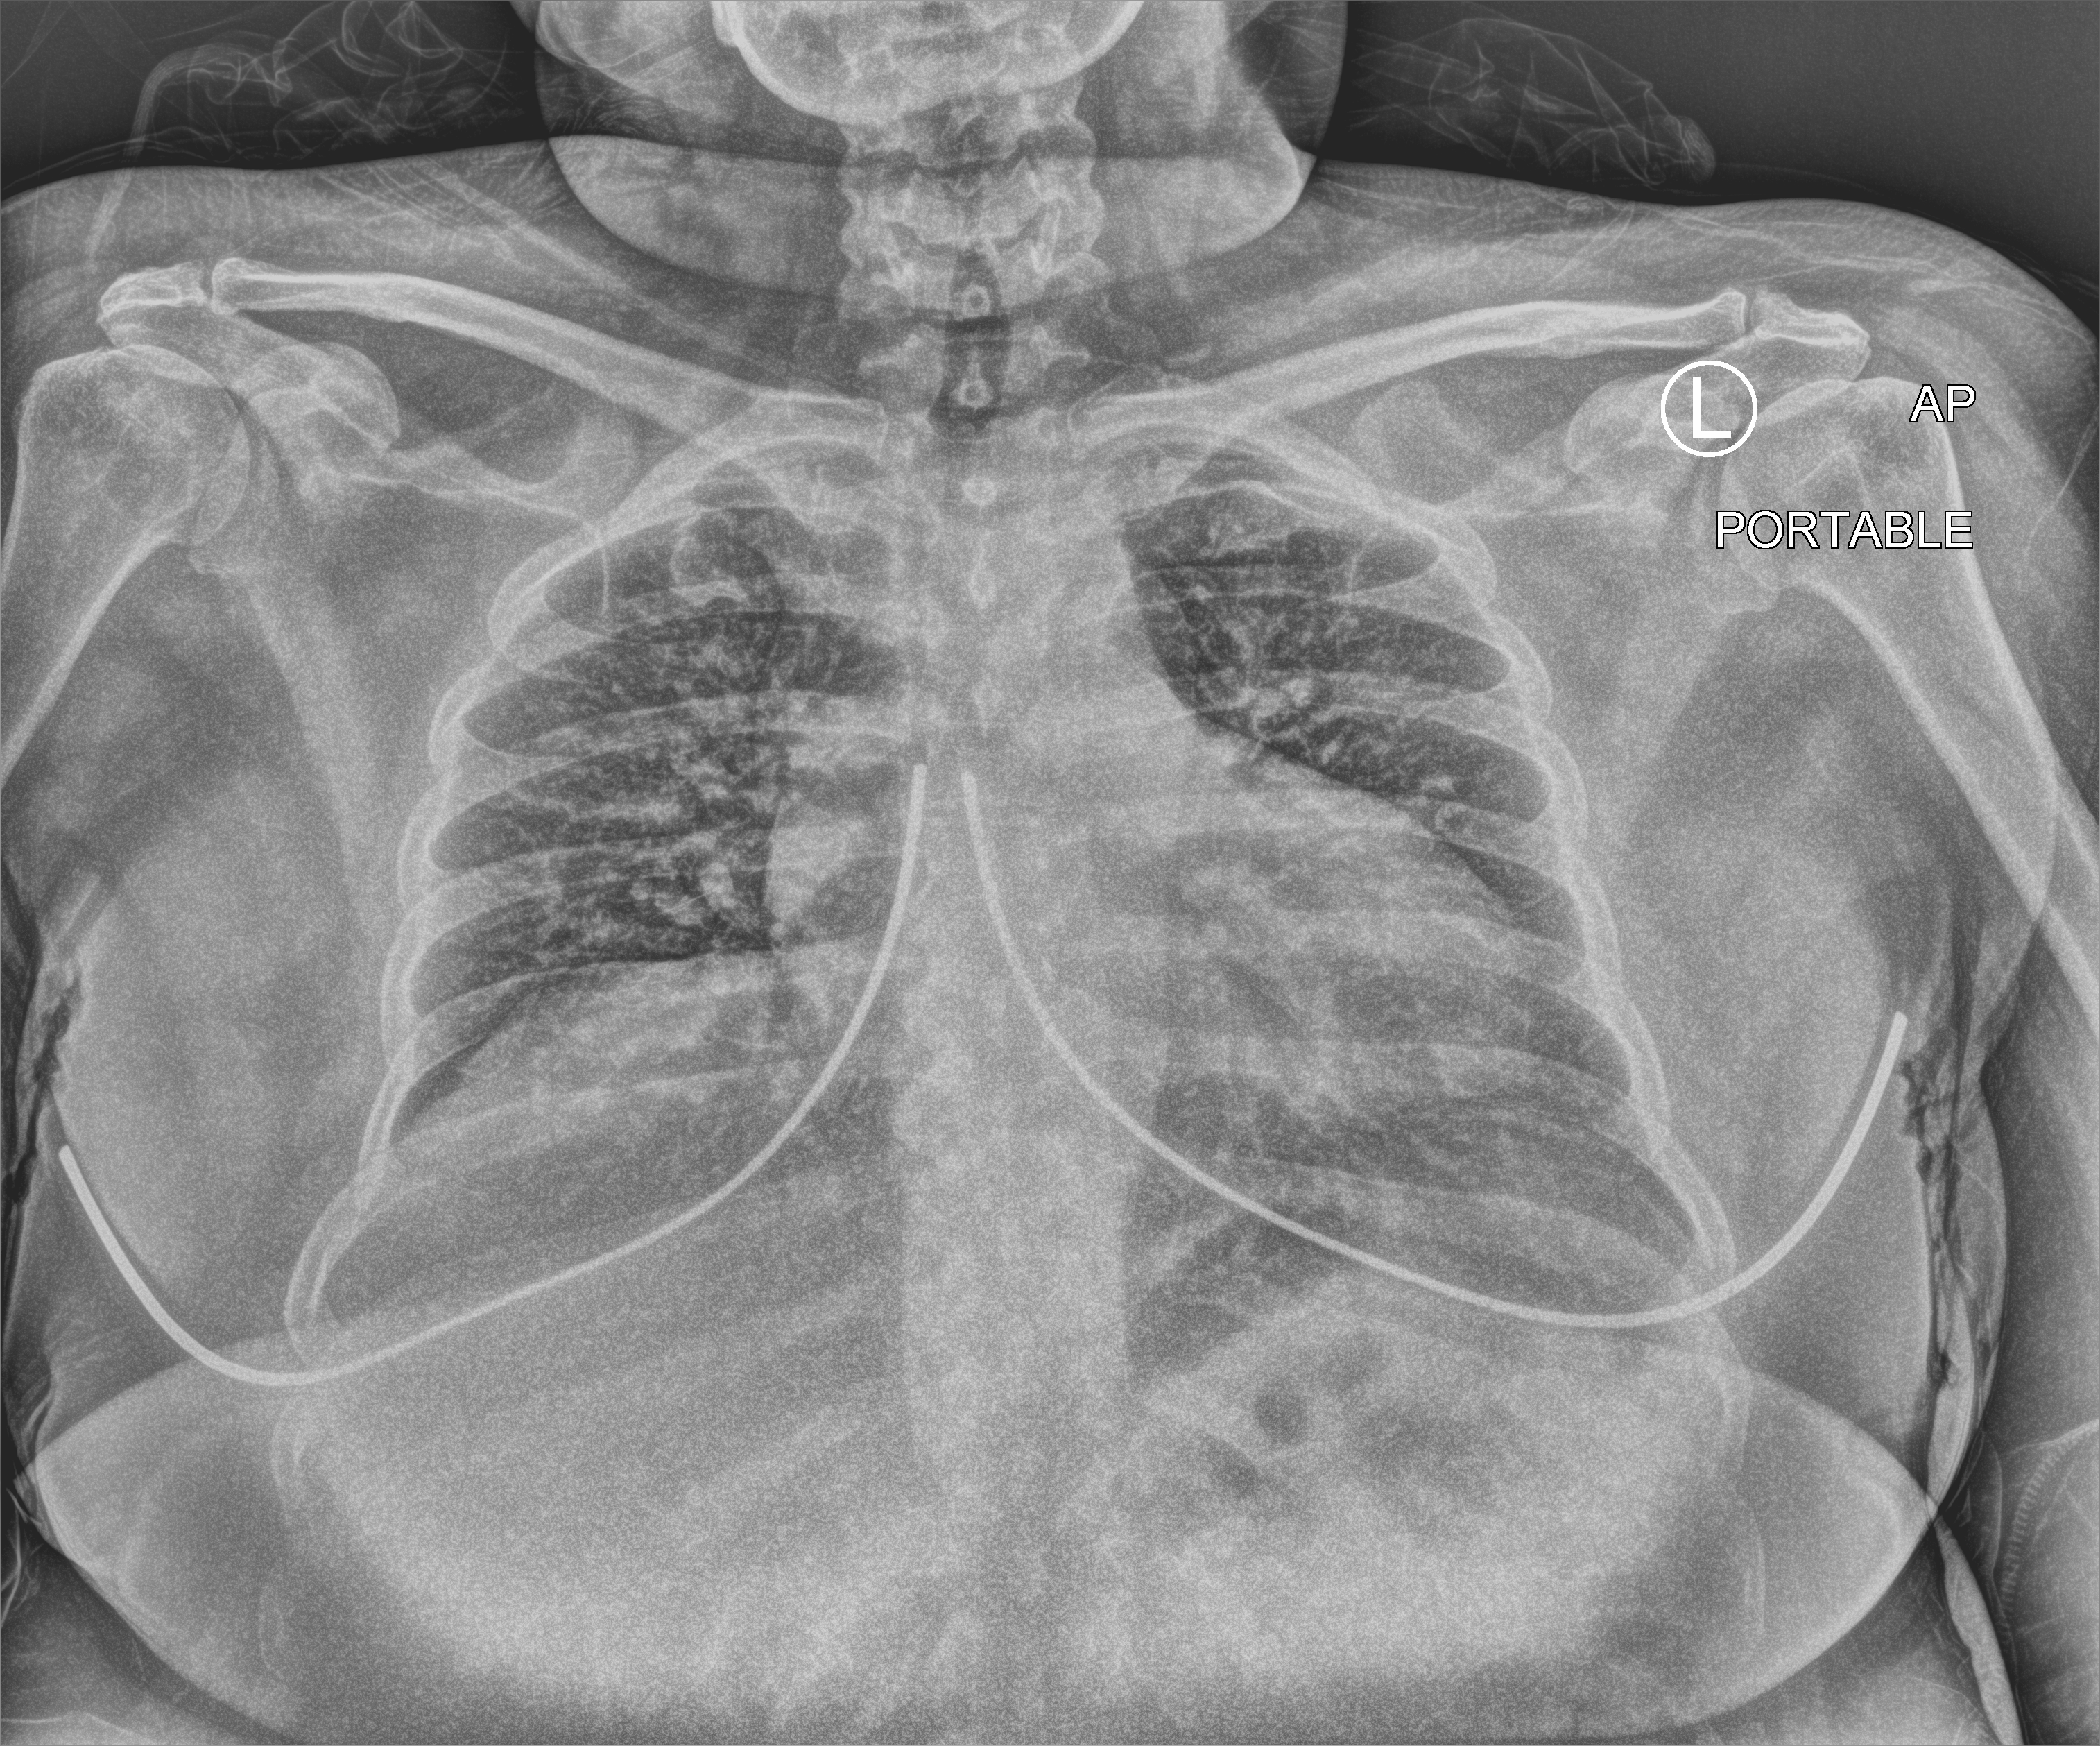
Chest X-ray (portable); anteroposterior (AP) projection. Patient hospitalised with COVID-19; female, aged 18–59 years.
Hospital-stay facts (about this admission, not read from this image; timing relative to this image not recorded): mechanically ventilated during this hospital stay: no.